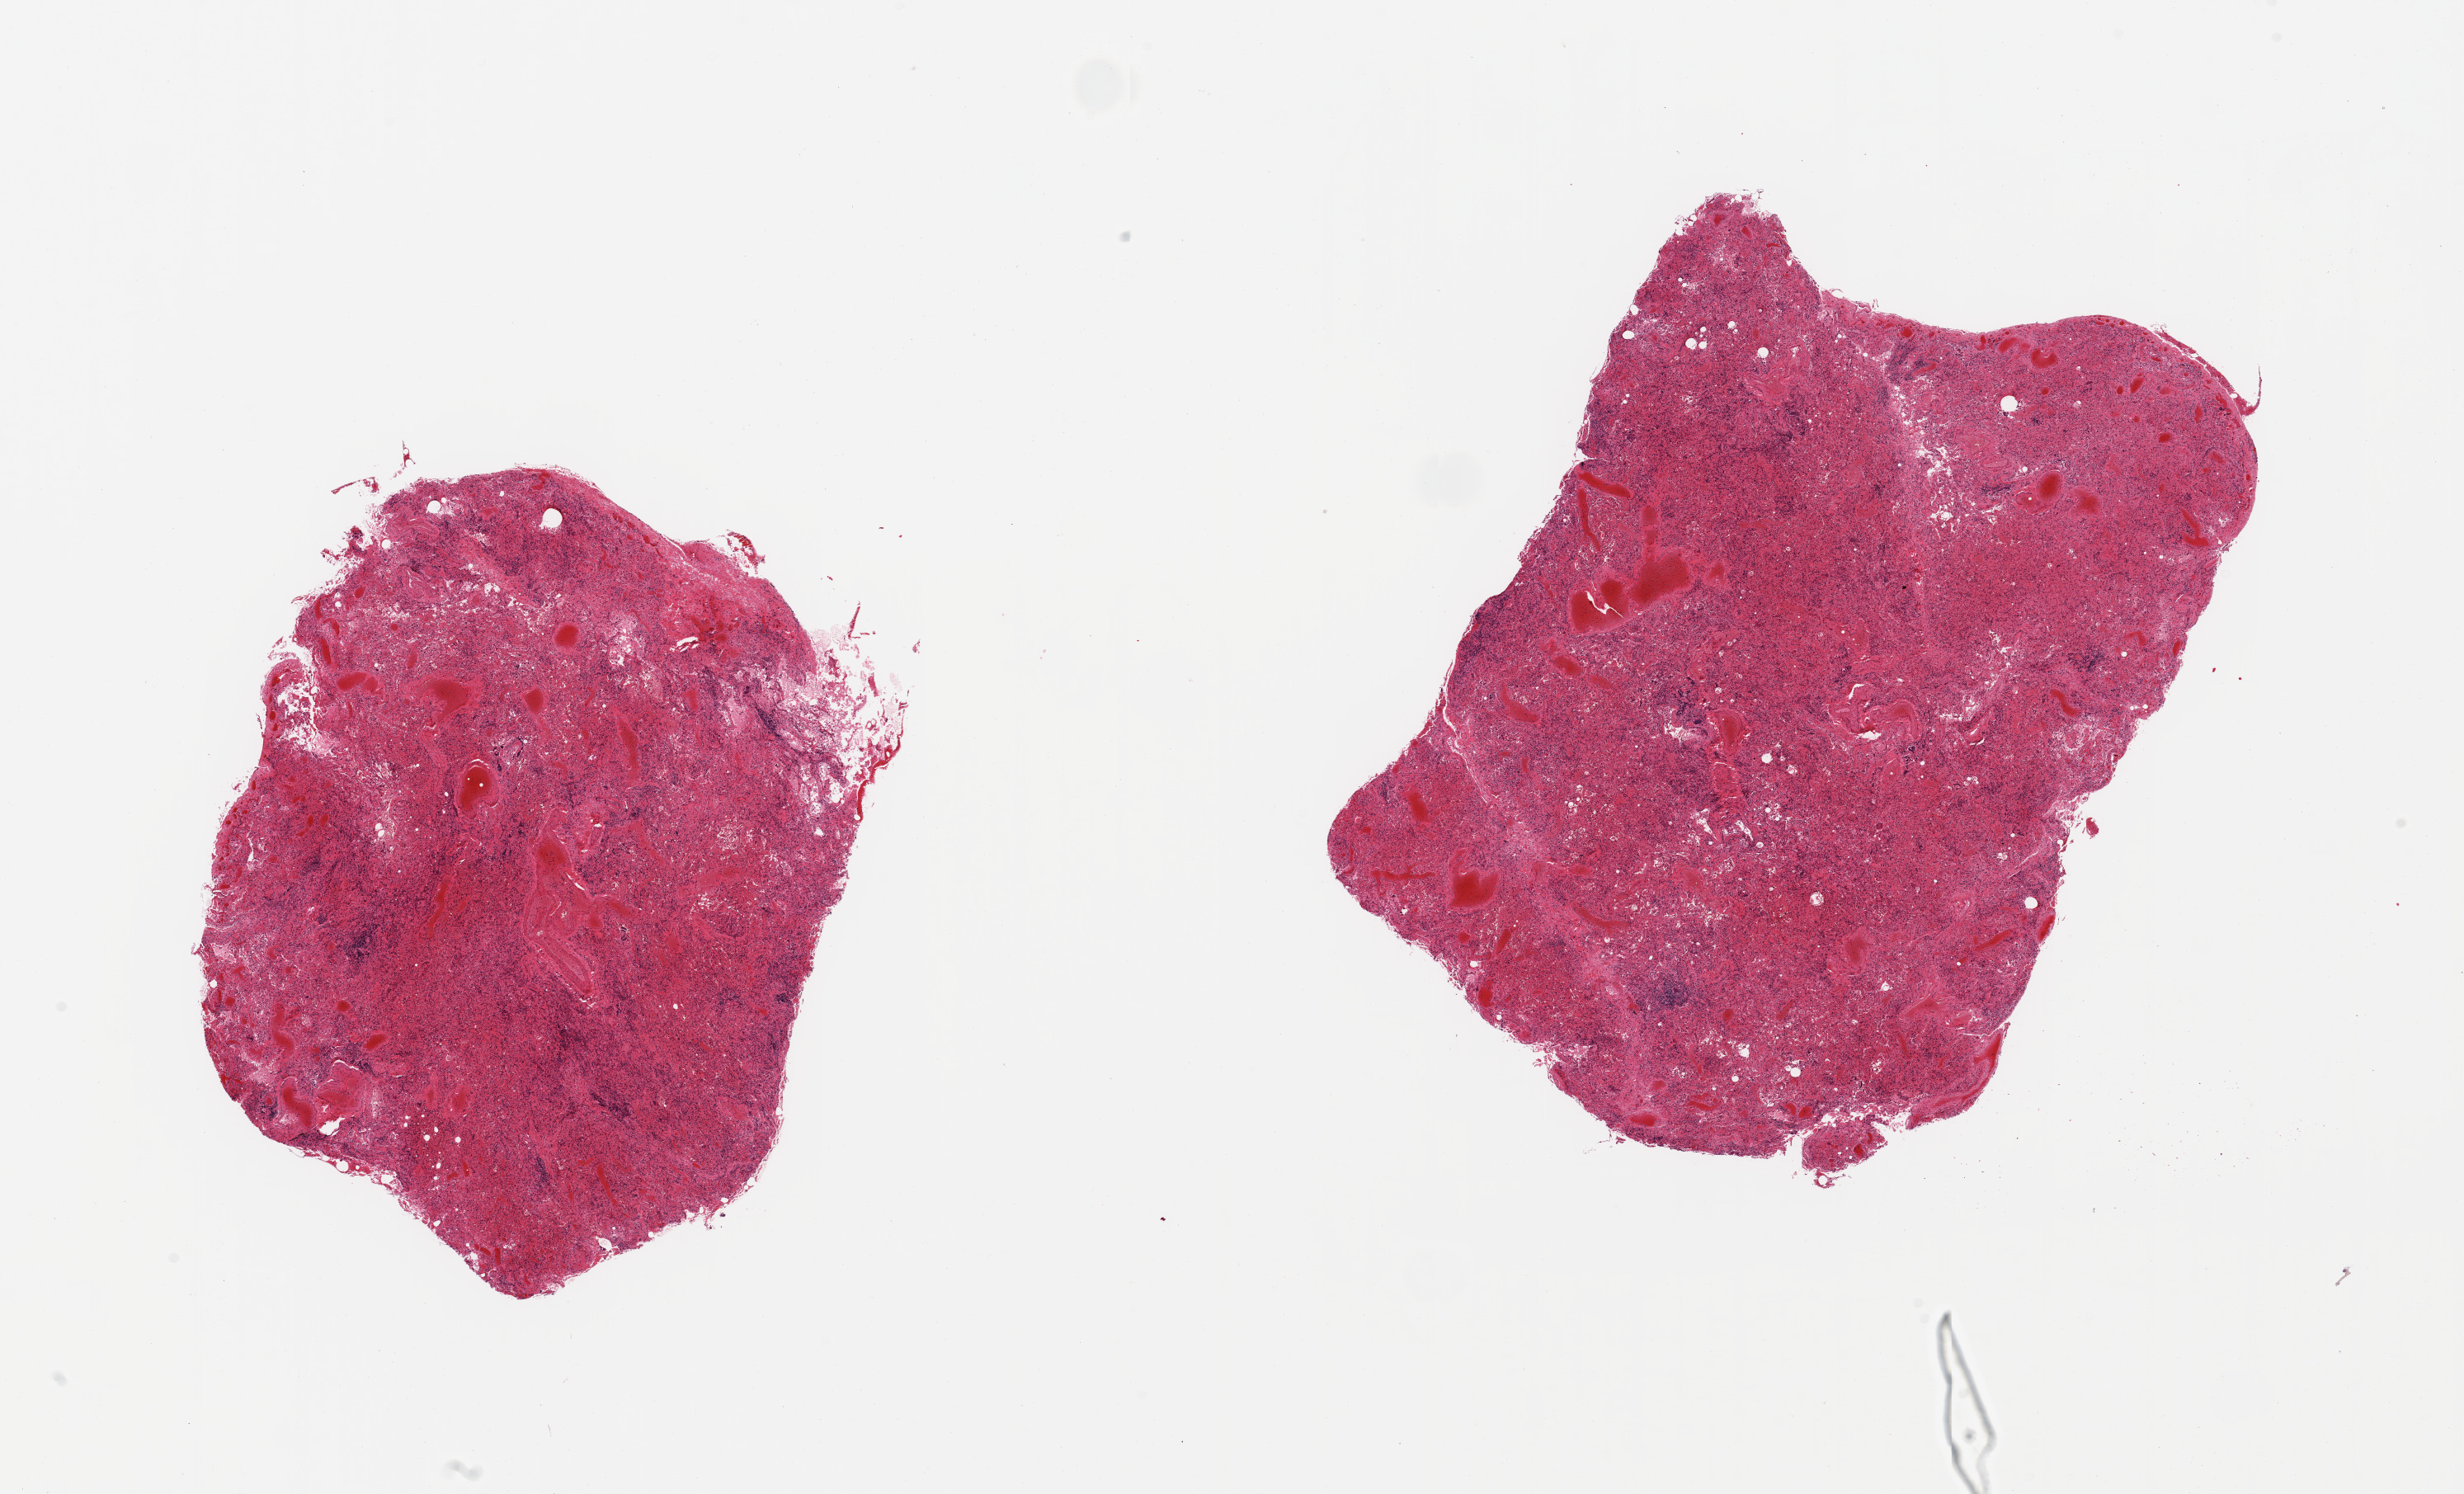
Digitized haematoxylin and eosin-stained section, brightfield — shown as a low-resolution overview of the whole scanned area (about 23.6 x 14.3 mm, from a 20x scan). PAXgene-fixed, paraffin-embedded tissue. Target tissue: lung. Donor tissue sample. Male donor.
• review note (as recorded): 2 pieces; severe vascular congestion, numerous pigmented alveolar macrophages and alveolar giant cells